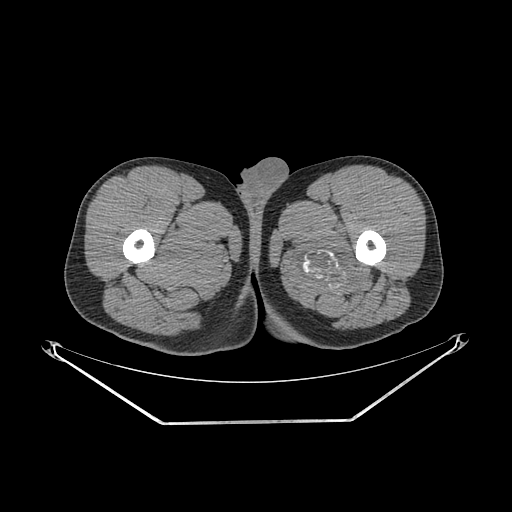
CT of an extremity soft-tissue mass (from a PET/CT study), one axial slice; position 256 of 267 along the scan axis; 140 kVp; soft-tissue window (W 400 / L 40 HU); 3.75 mm slice thickness; 512 × 512 image matrix, field of view 500 × 500 mm. Male patient. From the clinical record (not read from this slice): histological type: extraskeletal osteosarcoma; grade: high; site of the primary tumour: left adductur.
Structures marked on this image (expert contour drawn on MRI and transferred to this co-registered scan by the dataset authors):
- gross tumour volume (mass): box from (x=288, y=210) to (x=378, y=296) px